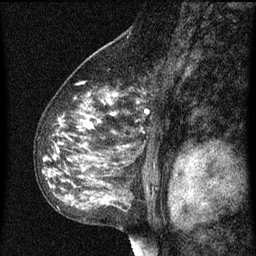
Breast MRI (dynamic contrast-enhanced), one sagittal slice. Dynamic contrast-enhanced series, image 2 of 3 at this slice position (ordered by acquisition). 1.5 T. TE 4.2 ms, TR 8 ms. 2 mm slice thickness. 256 × 256 image matrix, field of view 180 × 180 mm. Patient: female, 55 years.
Outlined on this slice (semi-automatically segmented with operator editing):
- analysis volume of interest (the breast-tissue region the enhancement analysis was run in; not a lesion): bounding box (x1, y1, x2, y2) in pixels: (42, 68, 157, 151)
- tumour enhancement mask (voxels above the 70 % enhancement threshold inside the analysis volume of interest): (56, 92, 149, 151)